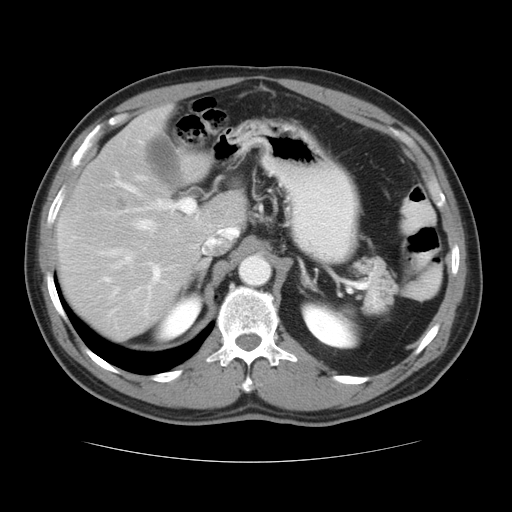
Contrast-enhanced abdominal CT, one axial slice; slice 23 of 37 in the series (ordered by position); reconstruction kernel STANDARD; 120 kVp; soft-tissue window (W 400 / L 40 HU); 512 × 512 image matrix, field of view 374 × 374 mm. Male patient, age 66 years. Case-level facts recorded for this patient, not image findings: diagnosis: colorectal cancer liver metastases, imaged before liver resection; multiple liver metastases: yes; largest metastasis: 1.6 cm.
Structures marked on this image (expert manual segmentation):
- hepatic veins: box from (x=101, y=176) to (x=235, y=267) px
- liver: (x=57, y=106)–(x=248, y=340)
- planned liver remnant (the part of the liver to remain after resection): (x=57, y=184)–(x=247, y=340)
- portal vein (with intrahepatic branches): (x=104, y=172)–(x=198, y=282)
- liver metastasis: (x=111, y=195)–(x=131, y=214)